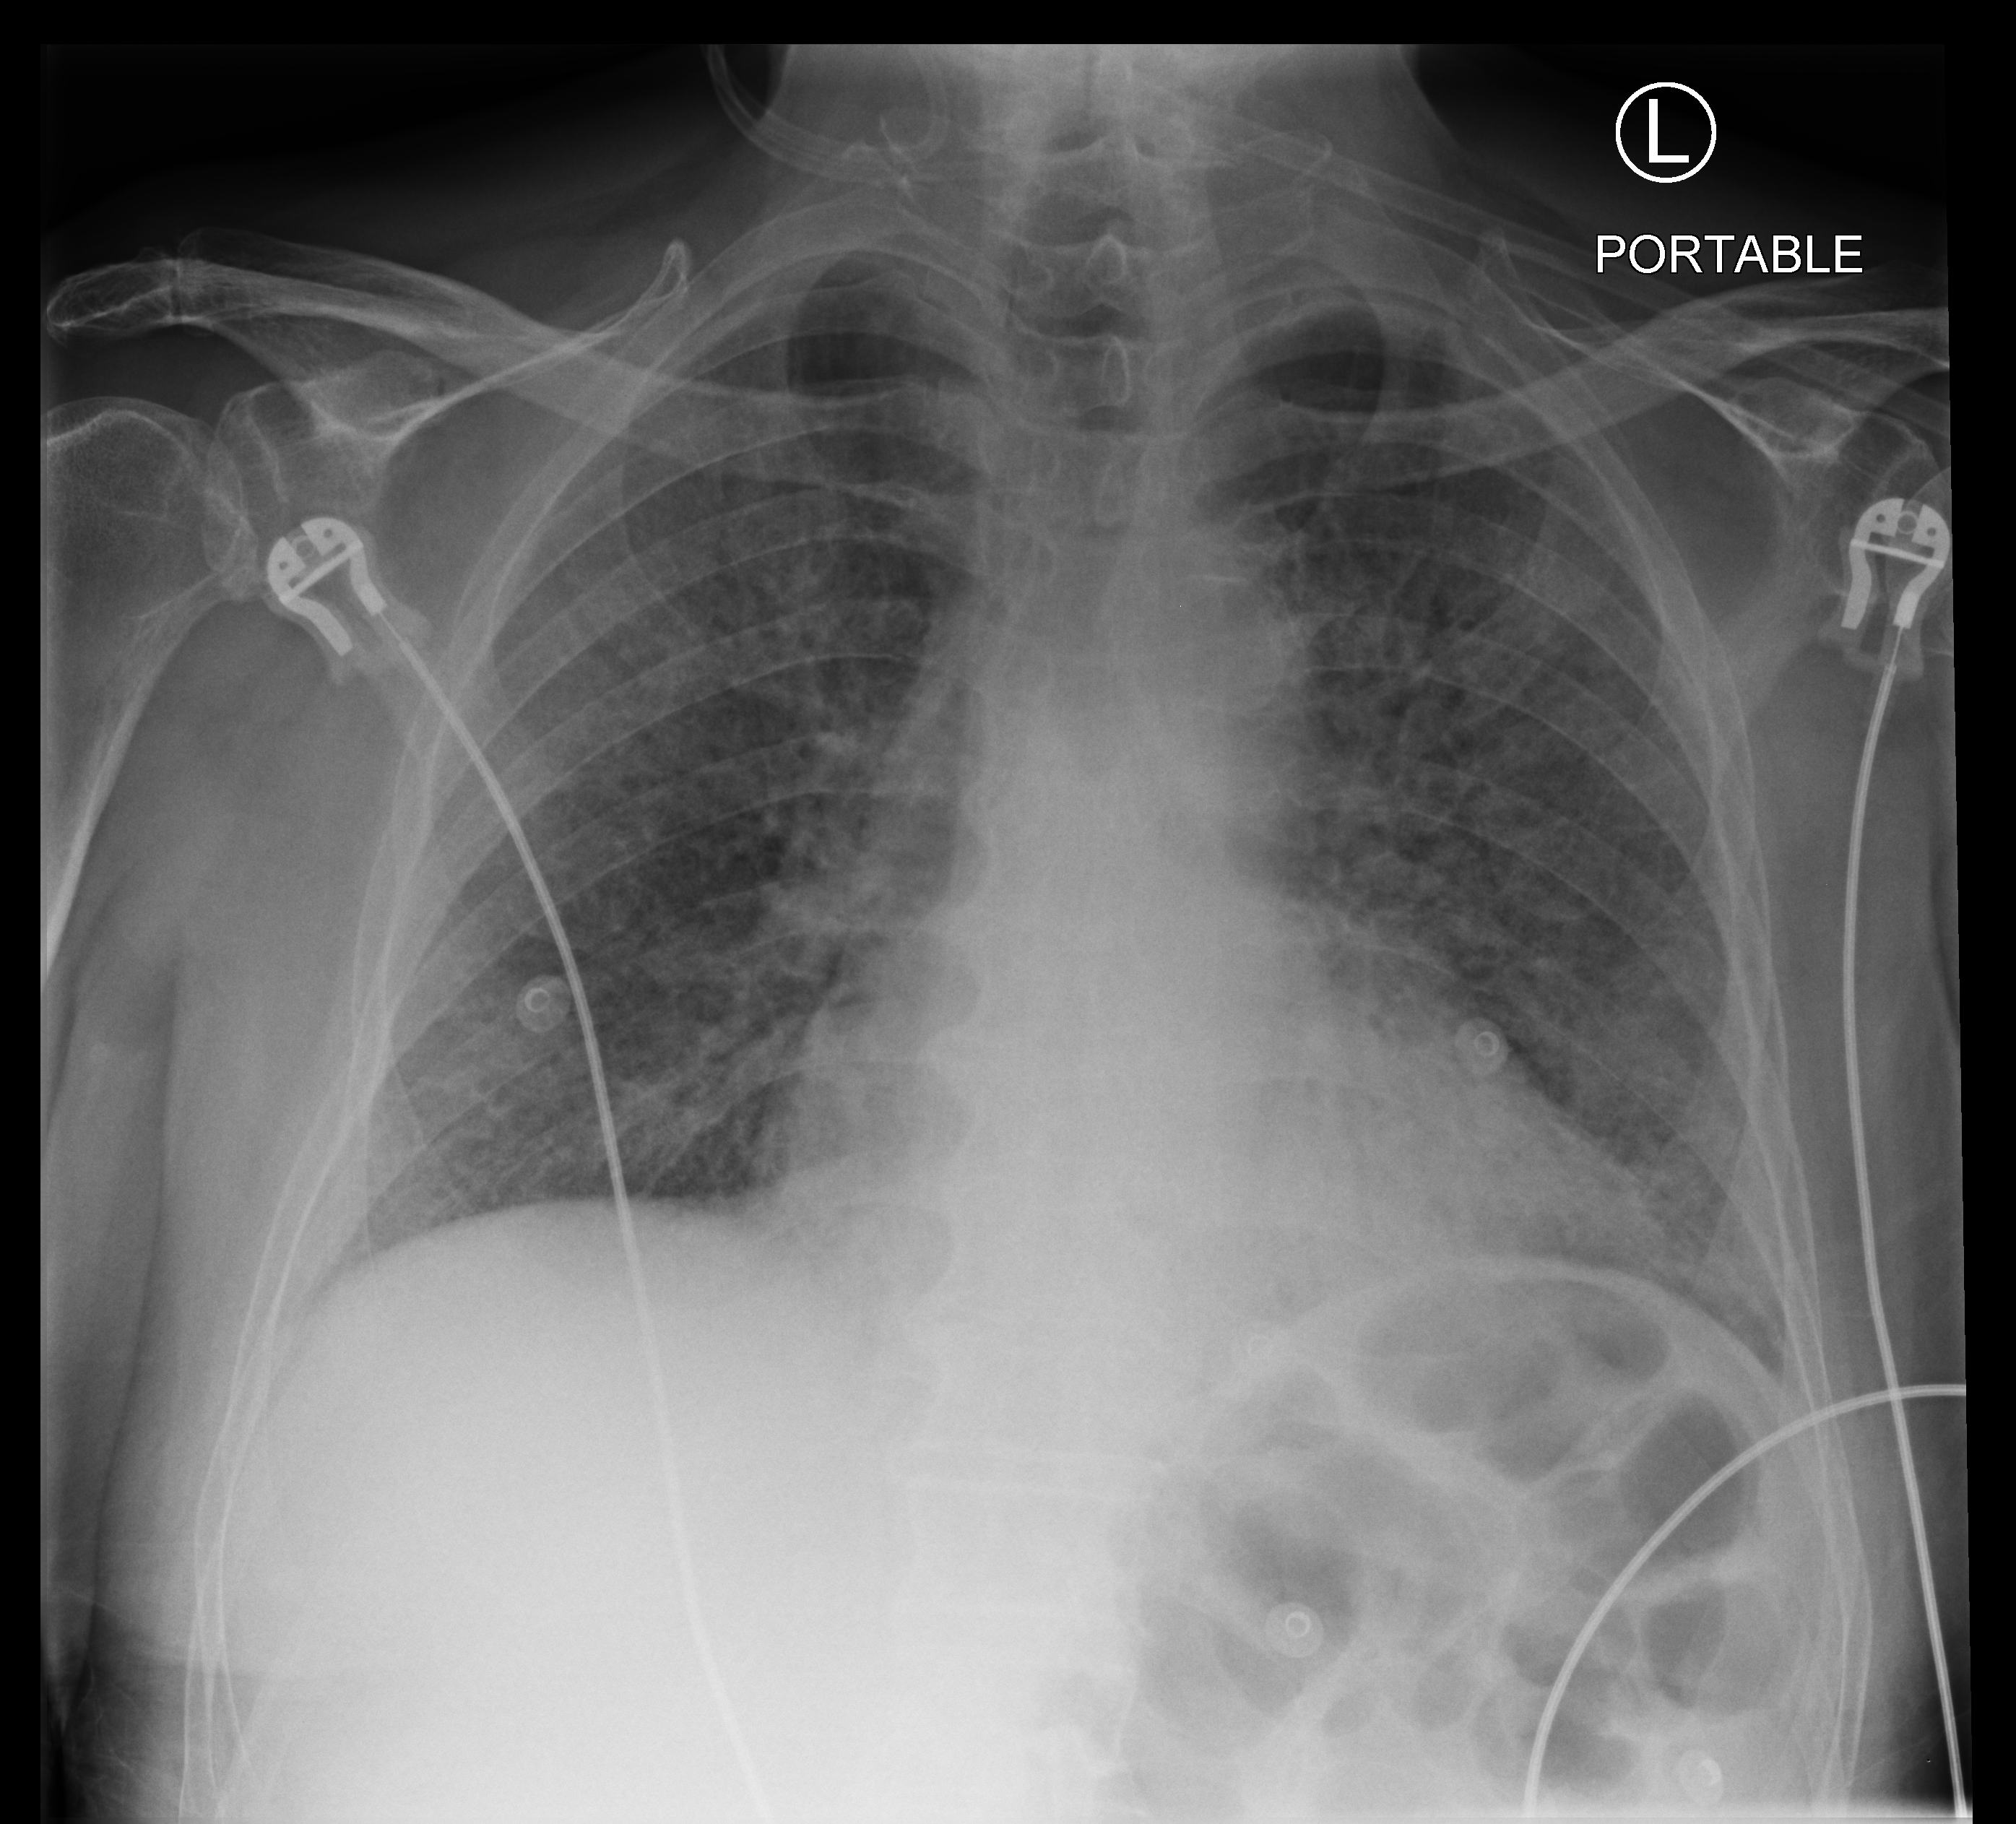
Bedside chest radiograph (computed radiography). Patient hospitalised with COVID-19; male, aged 75–90 years.
Hospital-stay facts (about this admission, not read from this image; timing relative to this image not recorded): length of hospital stay: 30 days; smoking status (admission record): never.